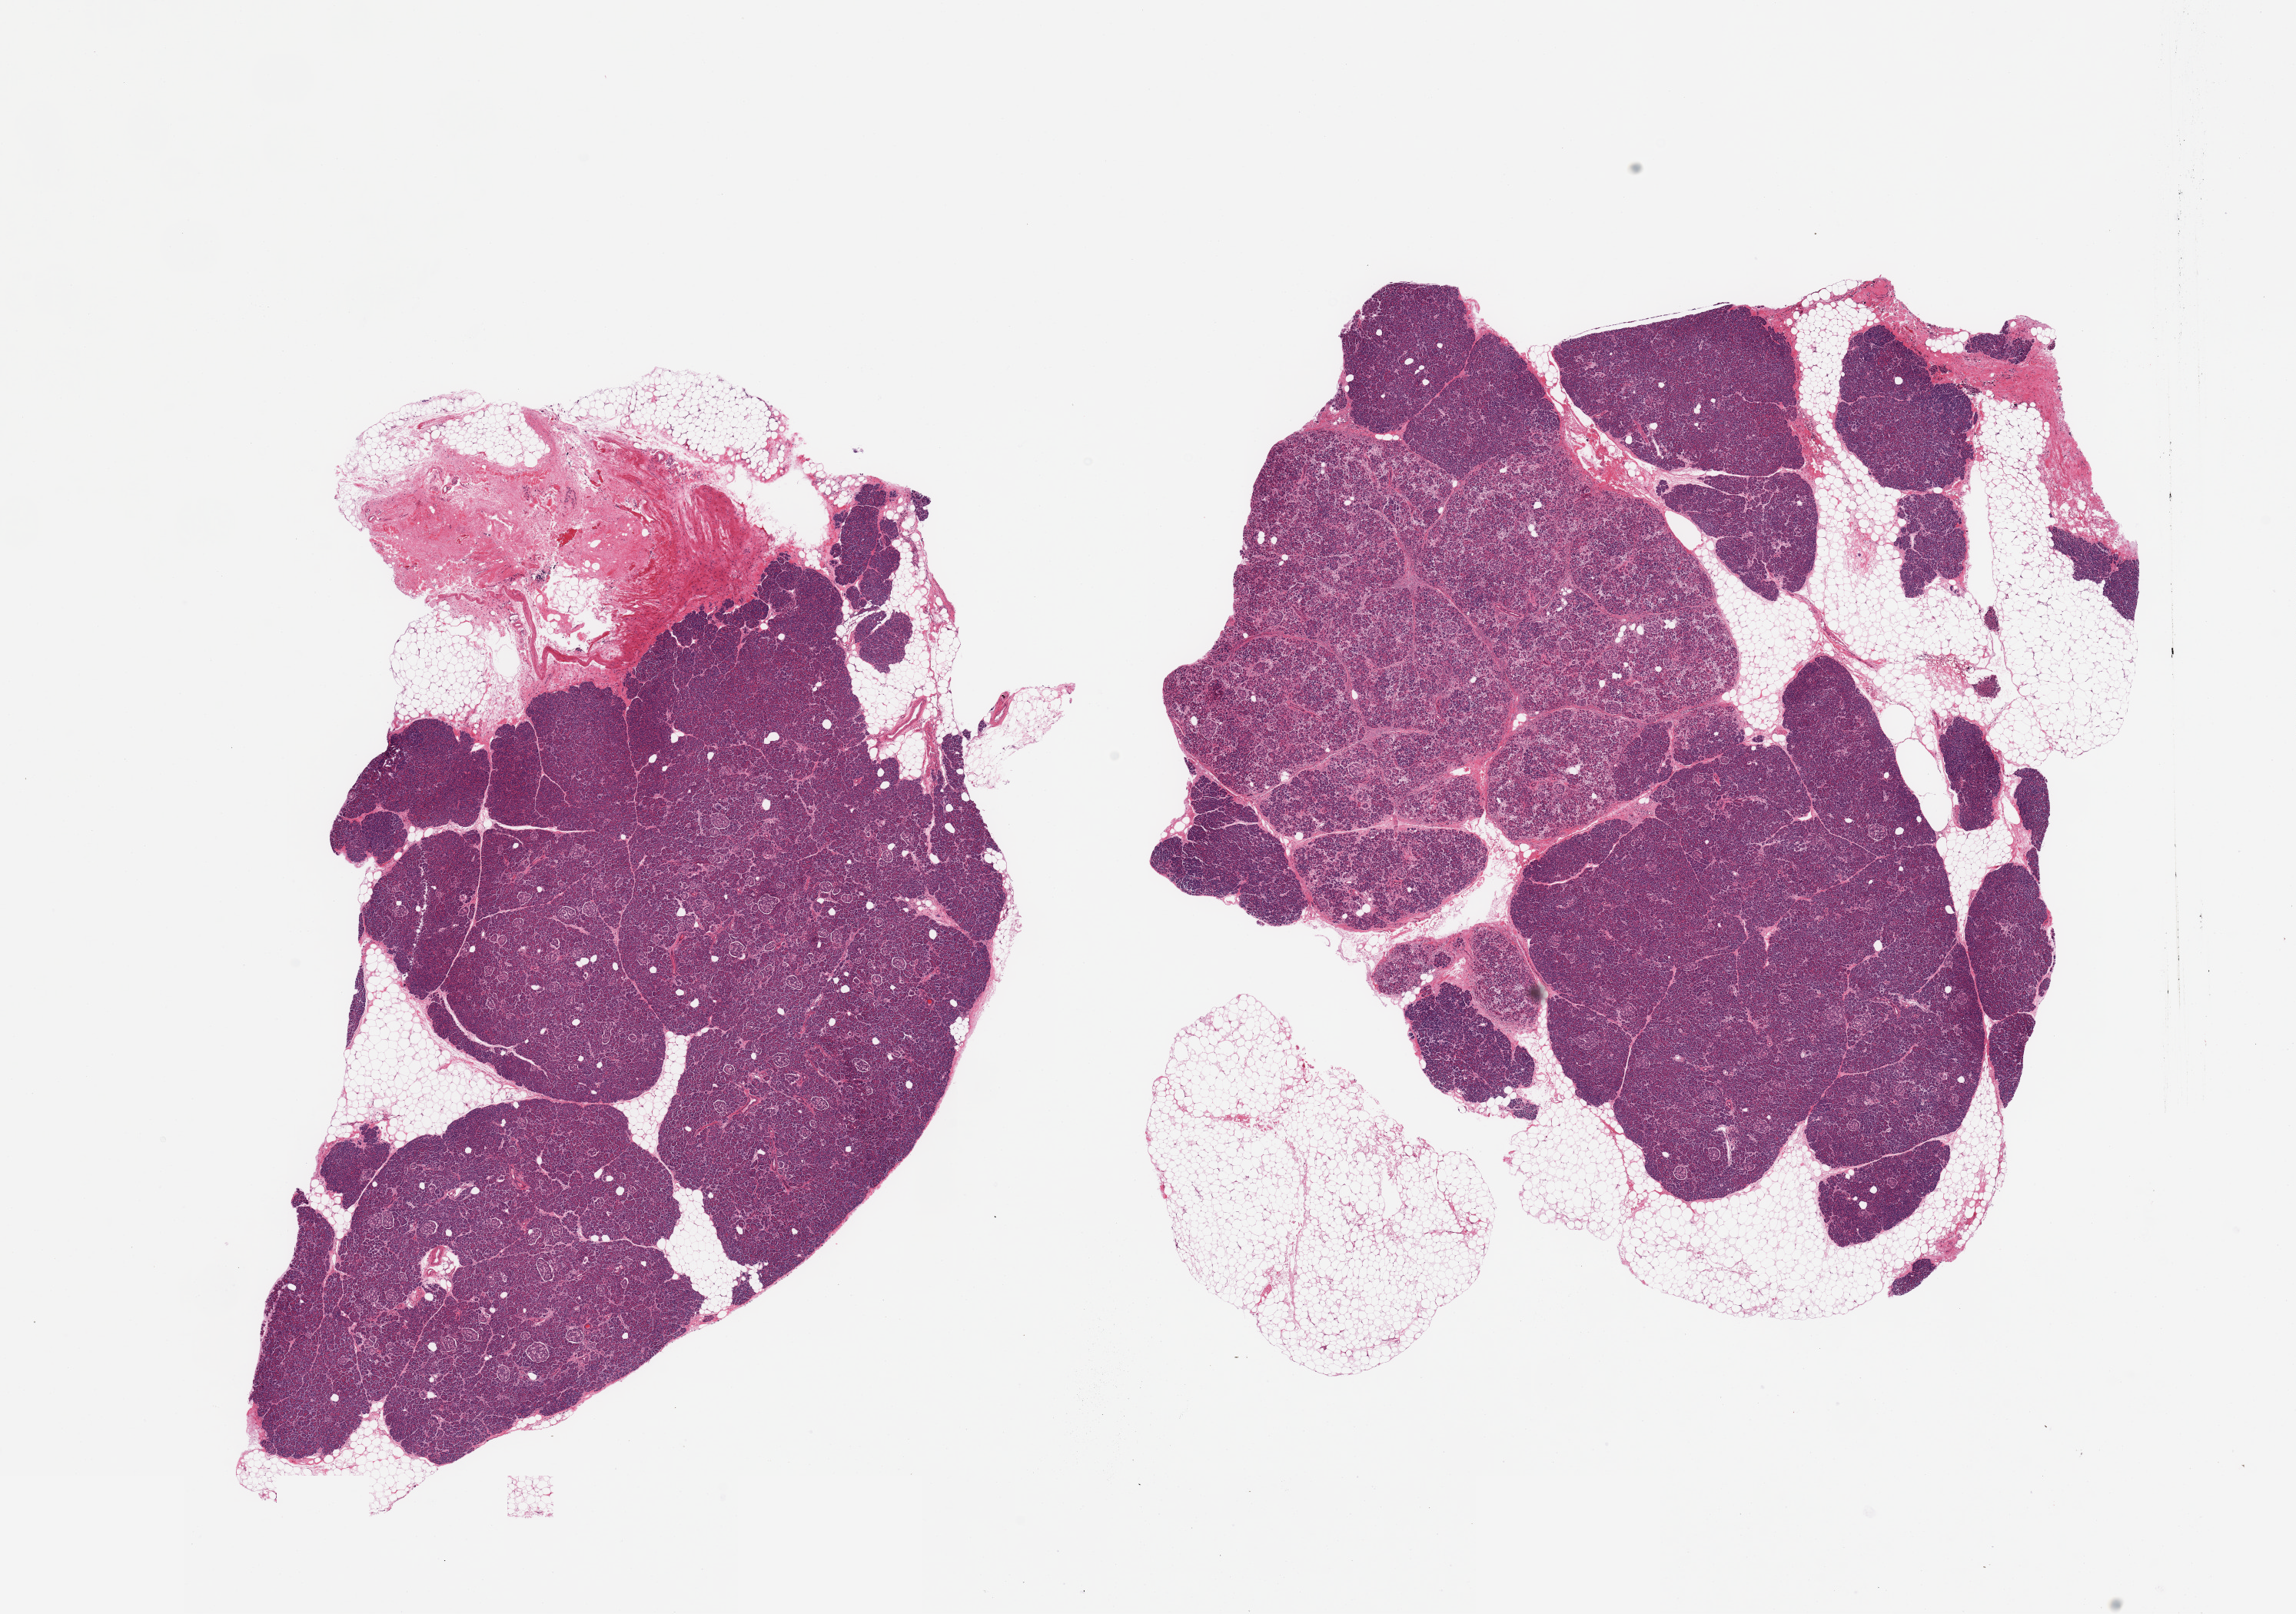
Digitized H&E-stained section — a low-resolution overview of the entire scanned area, about 23.6 x 16.6 mm; PAXgene-fixed paraffin-embedded (PFPE) section; target tissue: pancreas; tissue donor sample. Donor: female.
- reviewer comment on this tissue sample: 2 pieces, variable saponification; ~70% score 1; rest score 2; Numerous well -preserved Islets